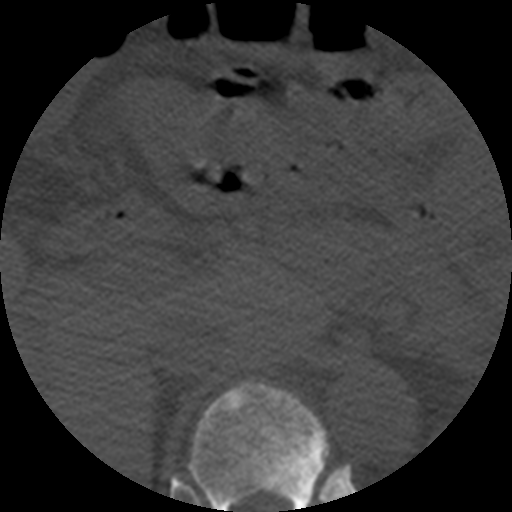
CT including the spine, one axial slice. Slice 249 of 508 in the series (ordered by position). Reconstruction kernel STANDARD. 120 kVp. Bone window (W 1800 / L 400 HU). 512 × 512 image matrix. Patient age 57 years. Case-level facts recorded for this patient, not image findings: primary cancer: prostate.
Outlined on this slice (semi-automatic segmentation, software-assisted and operator-edited):
- T11 vertebra: bounding box (x1, y1, x2, y2) in pixels: (189, 380, 329, 512)